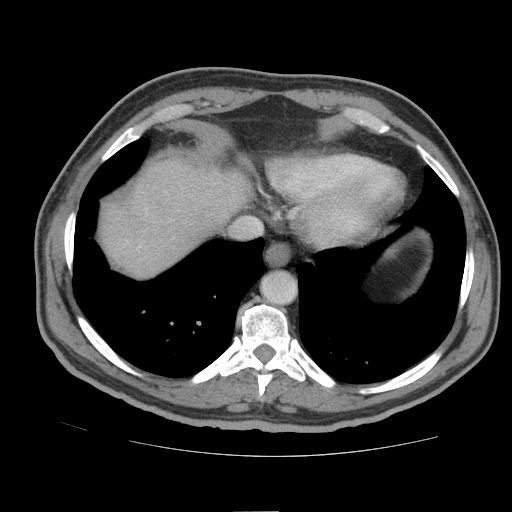
Contrast-enhanced abdominal CT (liver protocol), one axial slice; position 78 of 105 along the scan axis; soft-tissue window (W 400 / L 40 HU); 512 × 512 image matrix, field of view 380 × 380 mm. From the clinical record (not read from this slice): diagnosis: hepatocellular carcinoma (patient treated with transarterial chemoembolisation; whether this scan precedes or follows treatment is not stated here); TNM stage (as recorded): Stage-IIIB; Child-Pugh class: A; tumour nodularity: multinodular.
Structures marked on this image (semi-automatic segmentation, software-assisted and operator-edited):
- liver parenchyma outside the tumour (the mass and vessels are separate outlines, so this box may not span the whole liver): box from (x=100, y=158) to (x=250, y=276) px